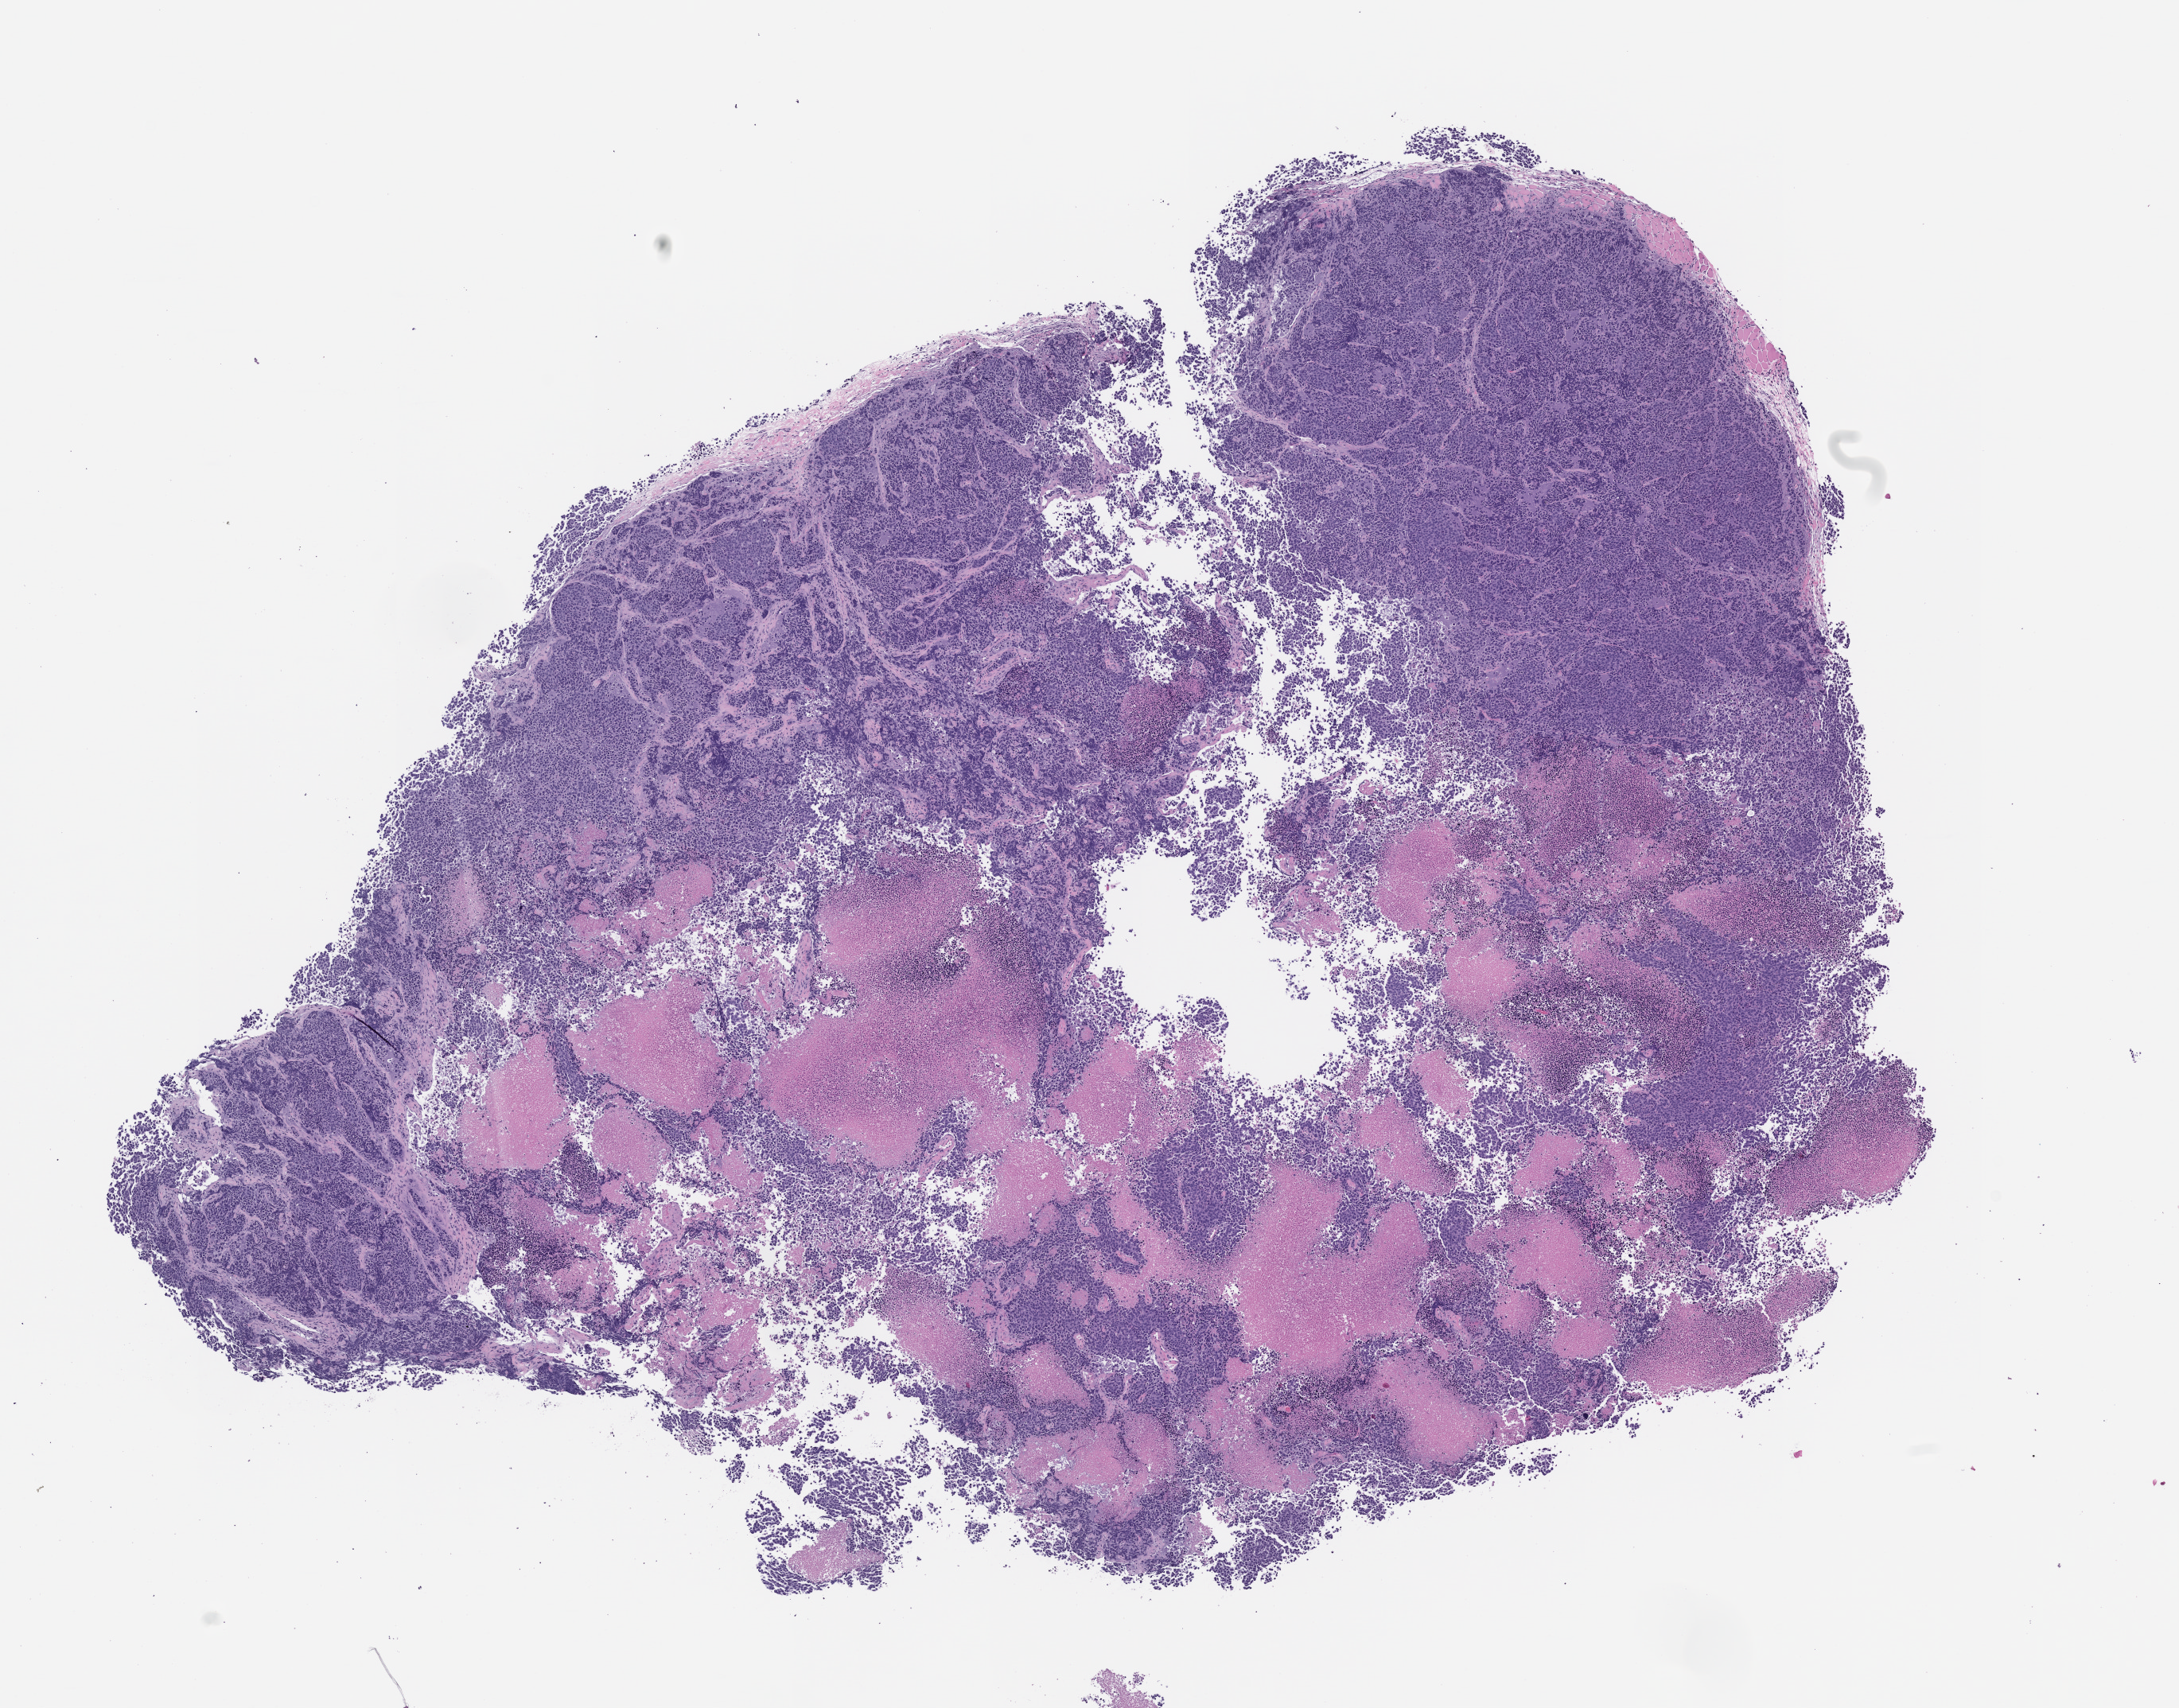
Hematoxylin and eosin (H&E) whole-slide image of a patient-derived xenograft (PDX) tumor grown in a mouse, passage 2, shown as a low-resolution overview of the whole scanned area (about 11.0 x 8.6 mm); FFPE section; originating tumor site category: neuroendocrine system.
• originating patient diagnosis: Neuroendocrine Carcinoma